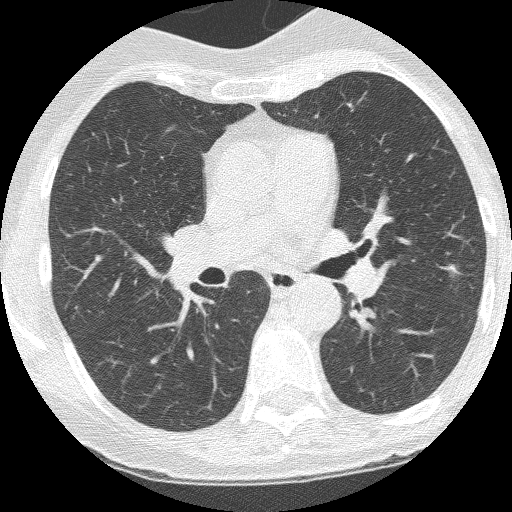
Chest CT (low-dose screening protocol), one axial image, third annual screen, lung window (W 1500 / L -600 HU), 1.25 mm slice thickness, slice 152 of 247 in the series. Female participant, aged 60 years at enrolment. Current smoker at enrolment.
- Lesion marked by an expert reader, box from (x=434, y=255) to (x=473, y=296) px.
- The screening reader recorded 2 non-calcified nodules or masses ≥4 mm on this exam; which of them this box marks is not recorded.
- Official screen result: positive, other.